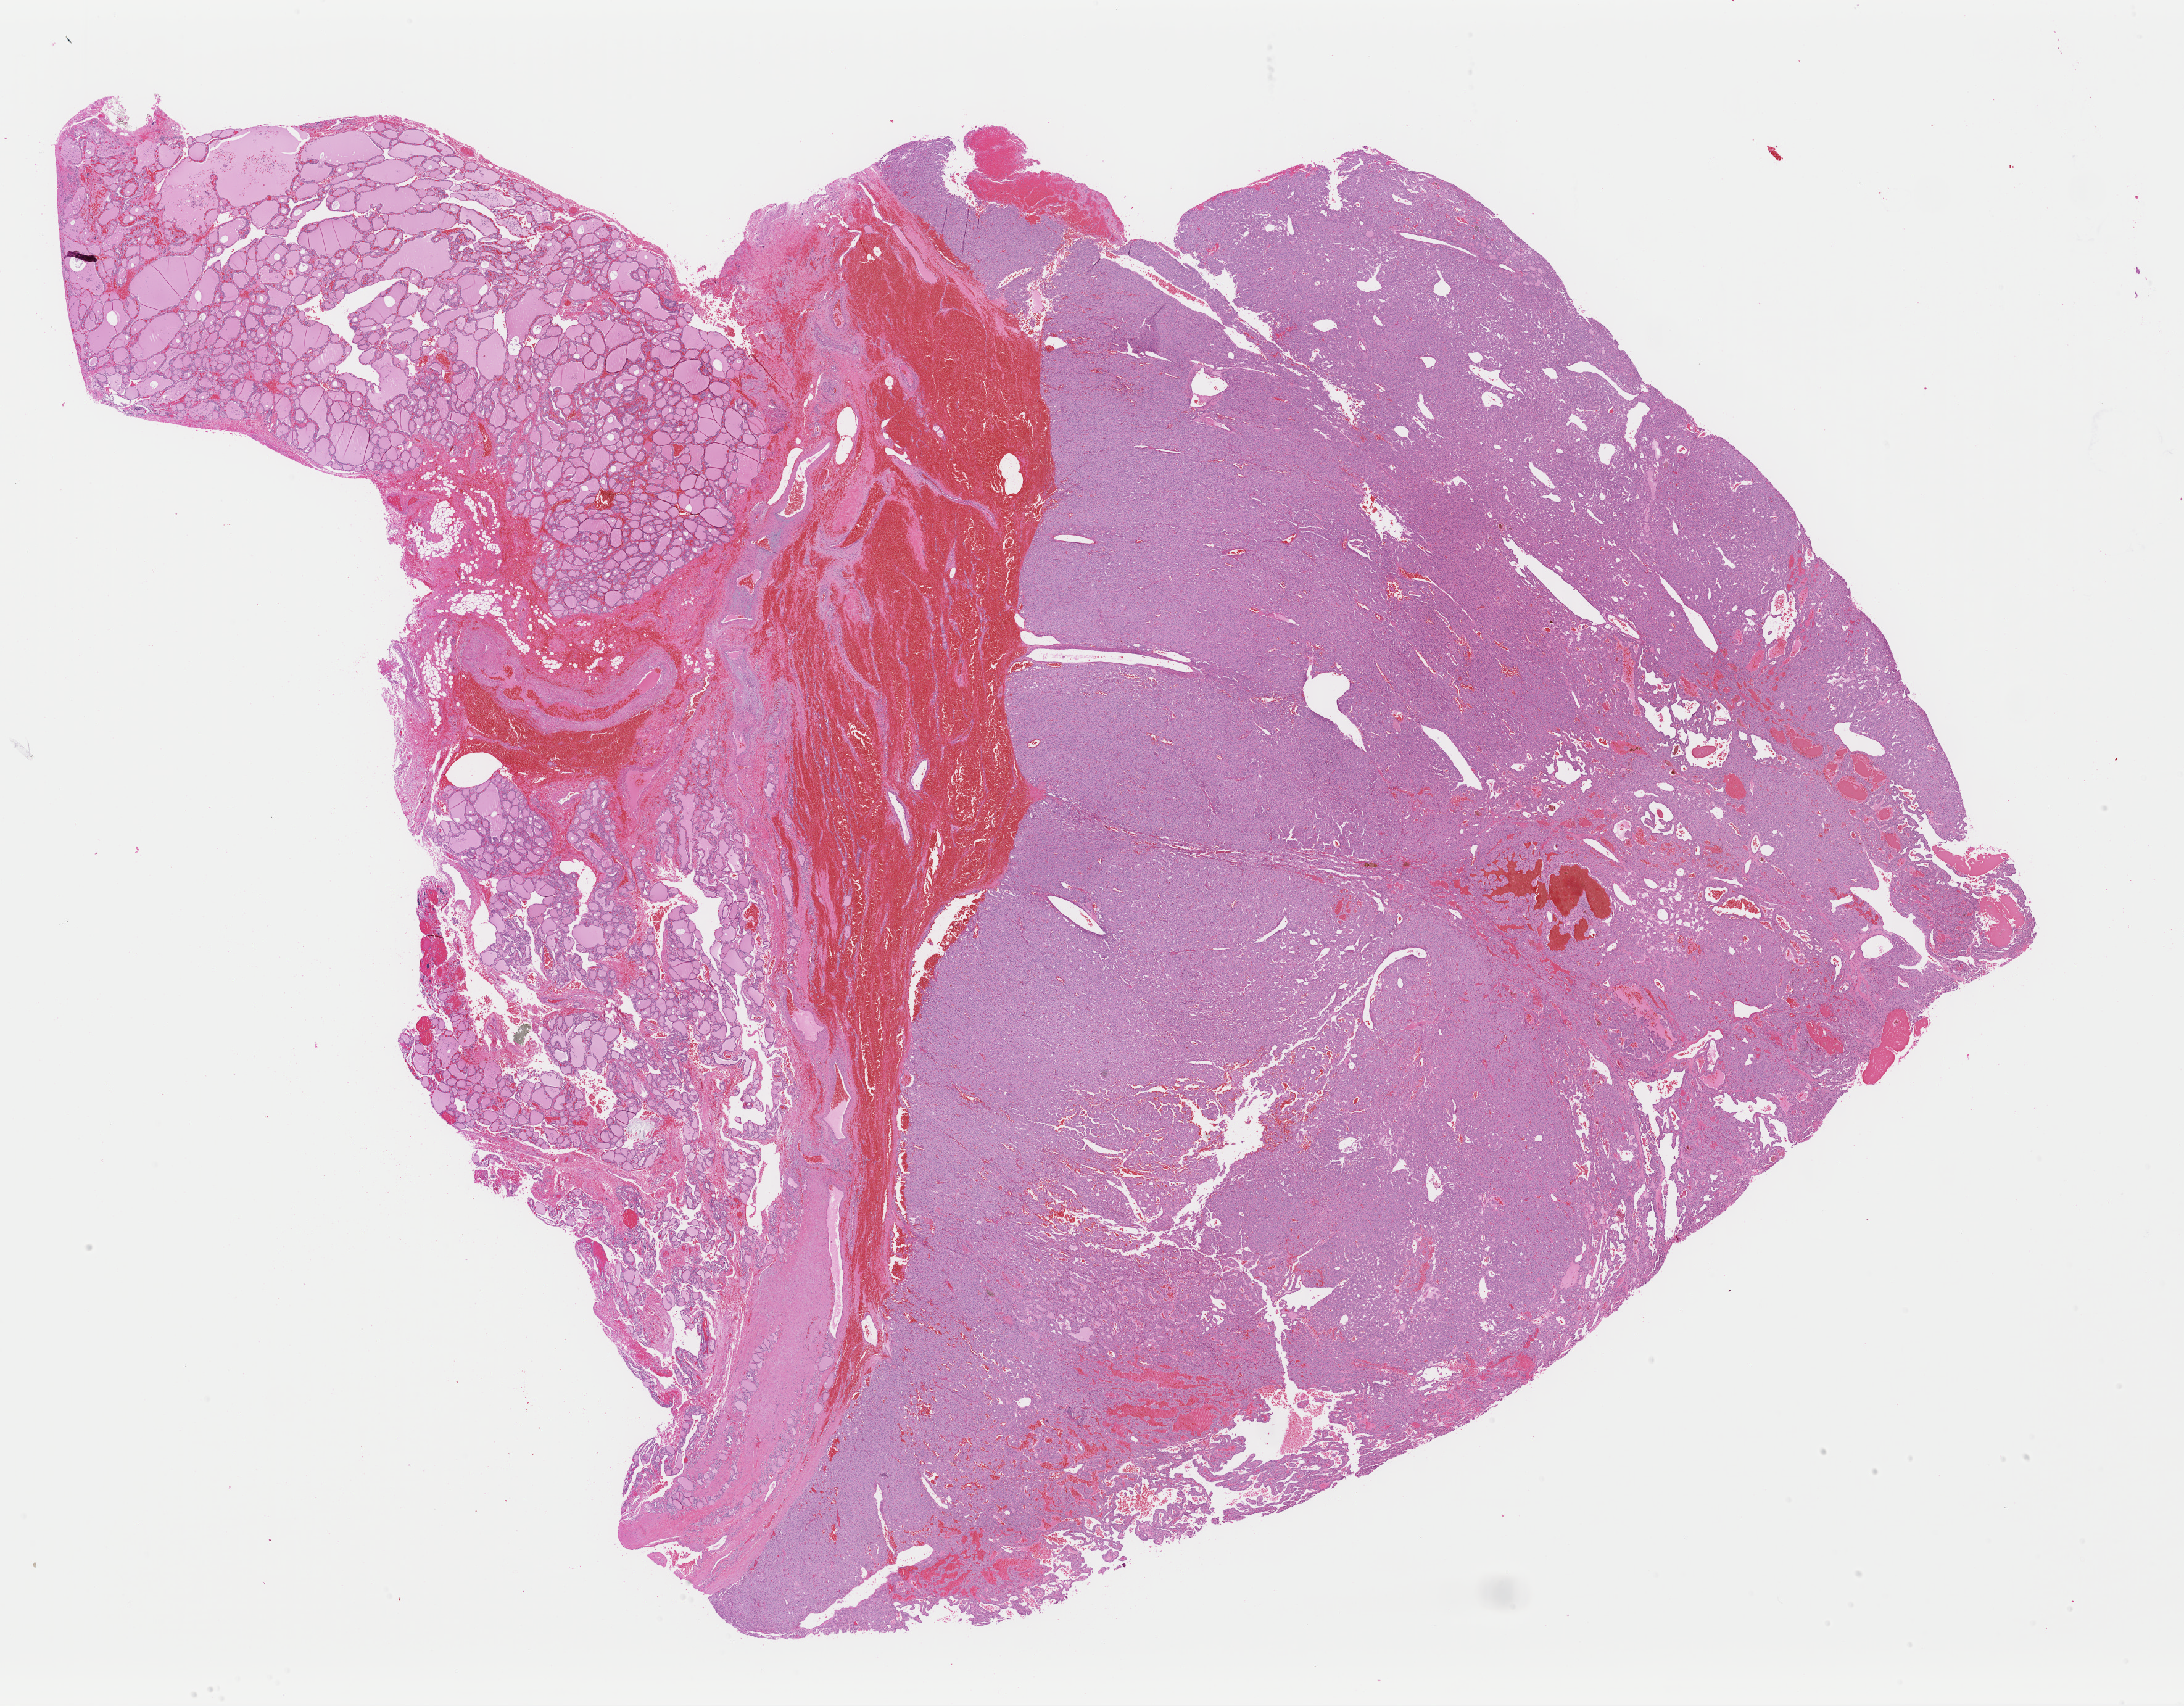
Digitized H&E tissue section (whole slide) — a low-resolution overview of the entire scanned area, about 28.0 x 21.8 mm (slide scanned at 40x), formalin-fixed paraffin-embedded (FFPE) diagnostic section, thyroid, primary tumour sample. Male patient; age at initial diagnosis 15 years.
Diagnosis: Papillary adenocarcinoma, NOS. Laterality: left. TNM: T3 N0 M0. AJCC pathologic stage: I (6th edition).